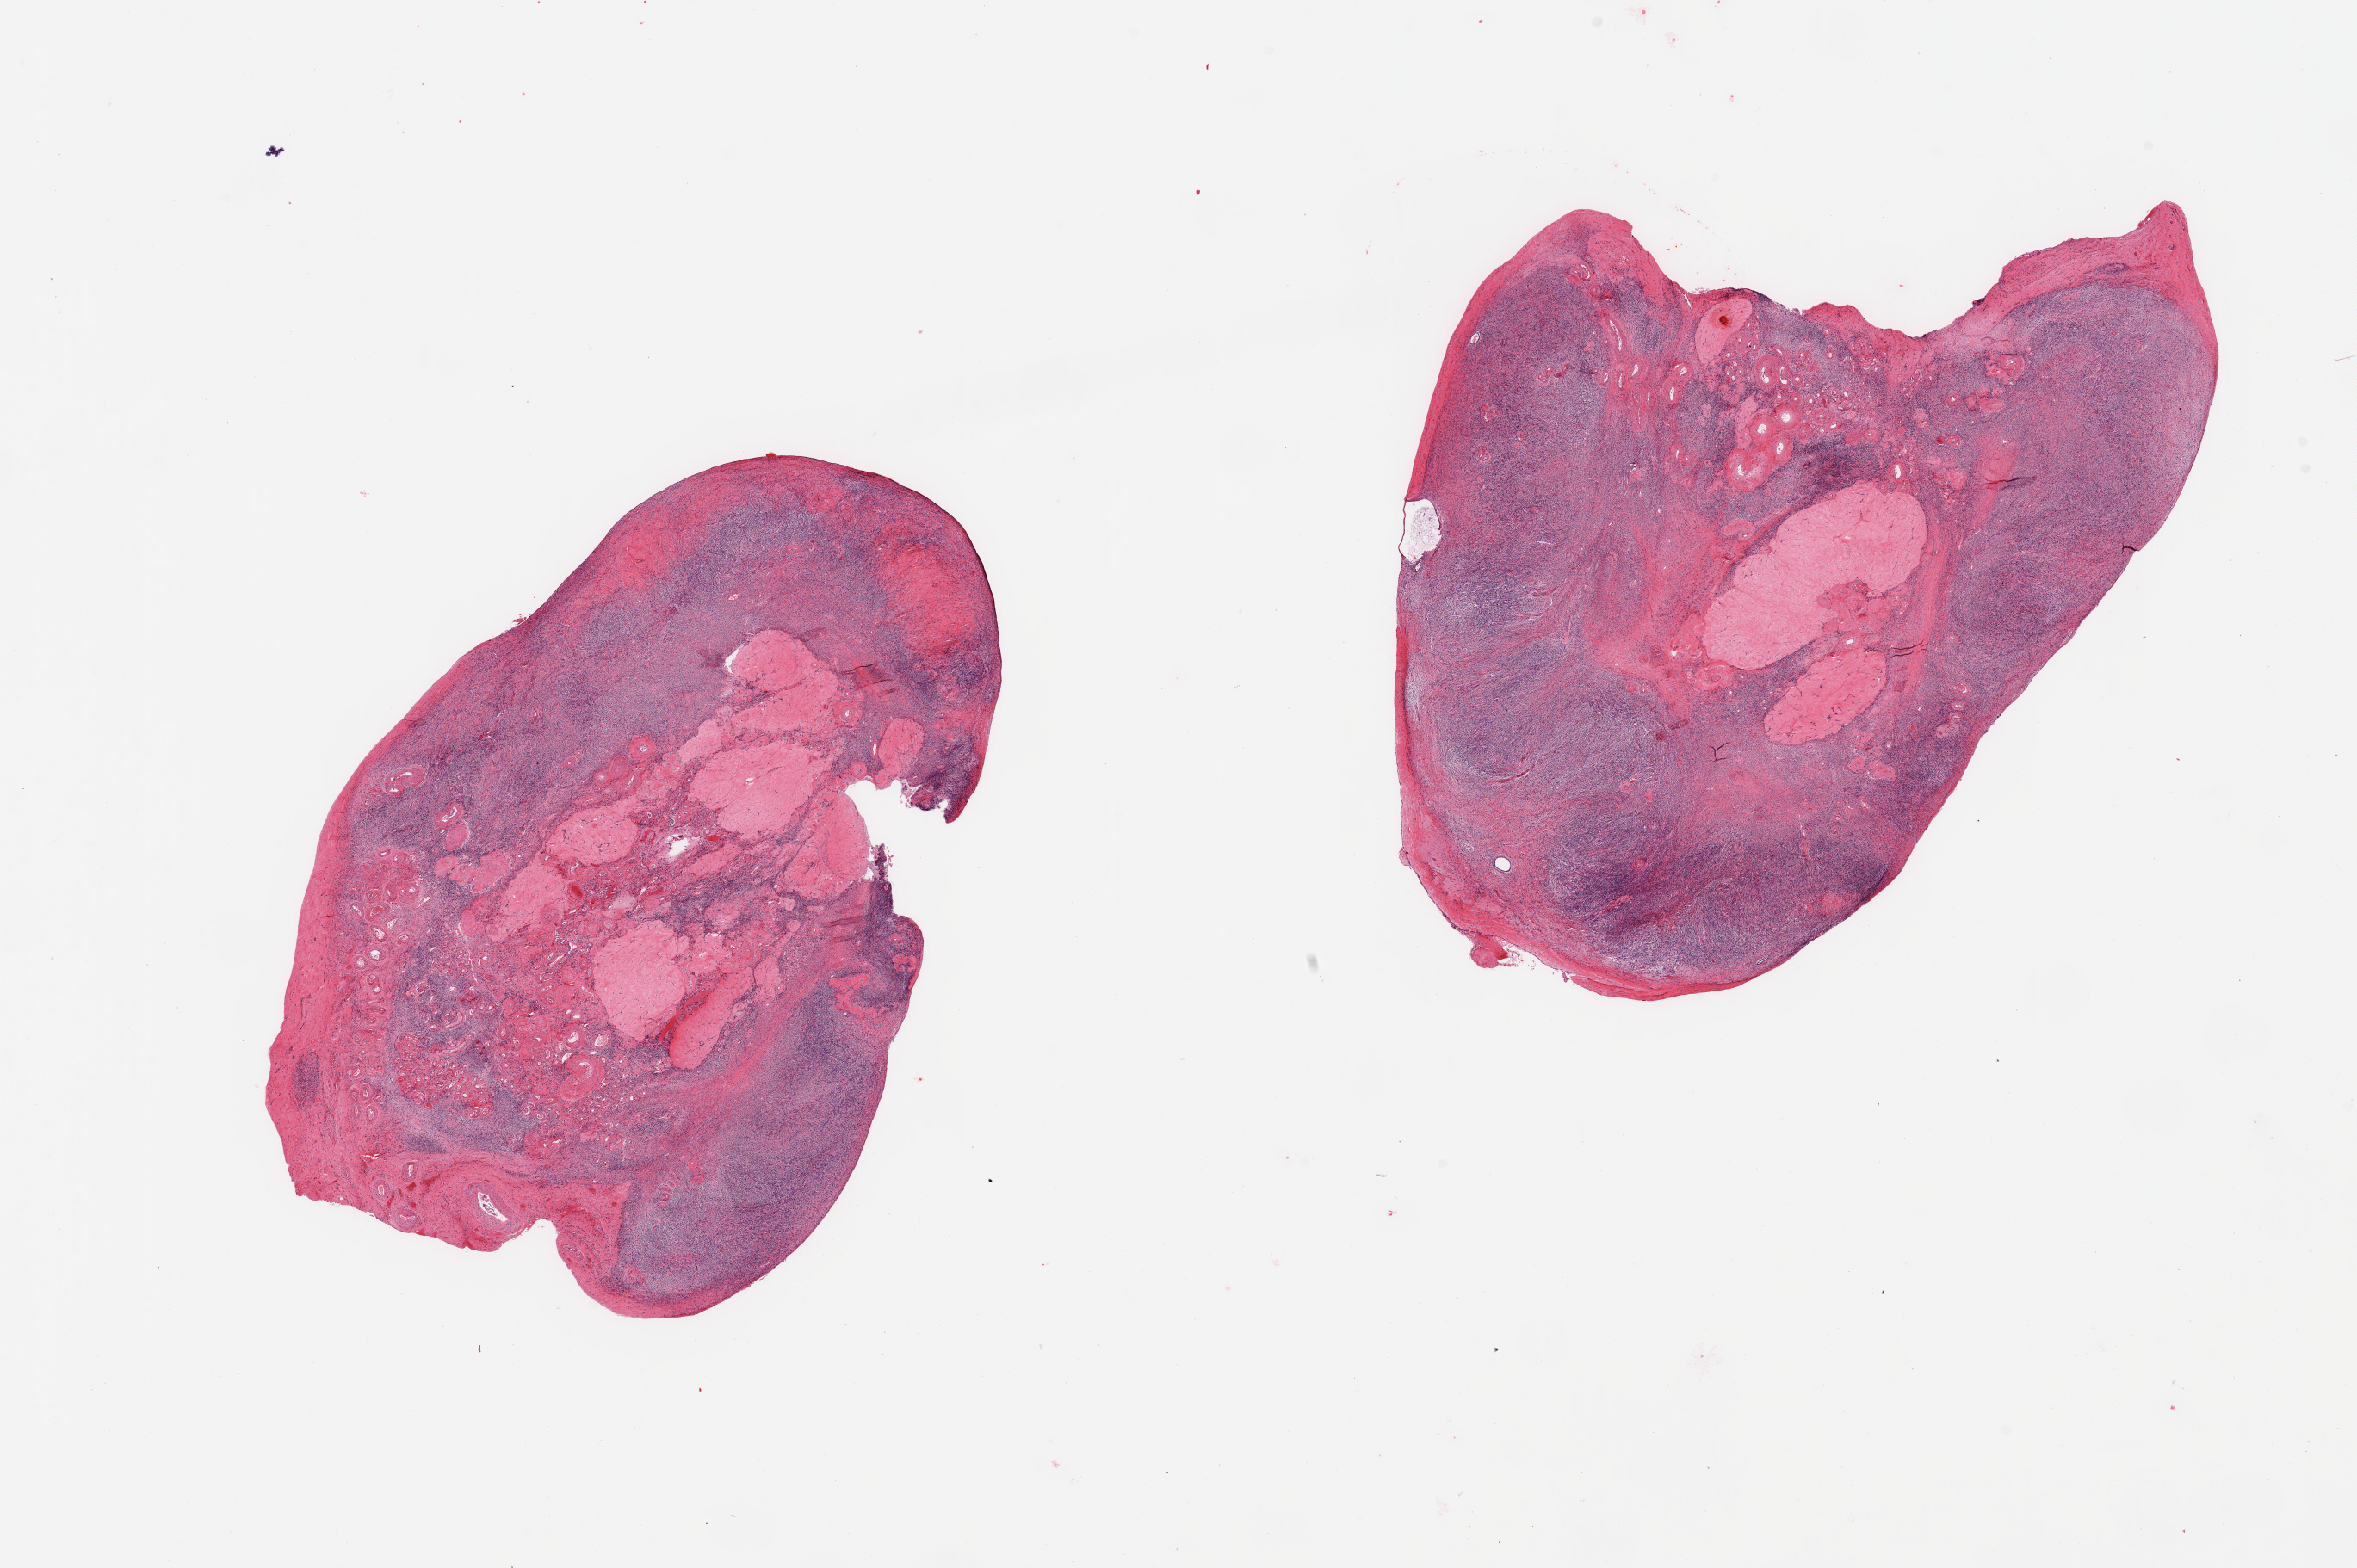
Whole-slide image, haematoxylin and eosin stain — whole scanned area (about 21.7 x 14.4 mm) shown as a low-resolution overview. PAXgene-fixed paraffin-embedded (PFPE) section. Sampled site (target tissue): ovary. Donor tissue sample. Donor: female.
- review note (as recorded): 2 pieces; atrophic with 10% & 20% corpora albicantia content